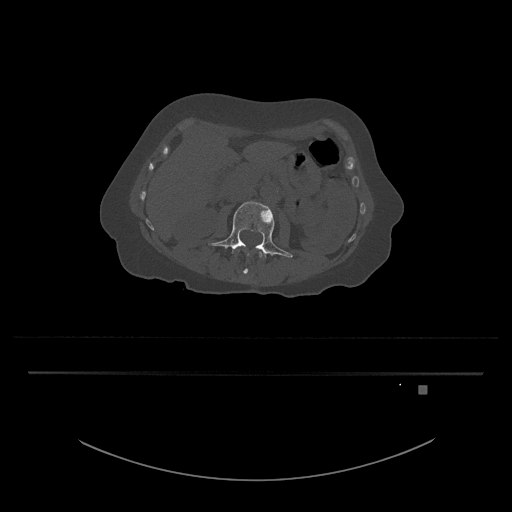
CT including the spine, one axial slice; position 437 of 797 along the scan axis; reconstruction kernel Br40s/3; bone window (W 1800 / L 400 HU); 0.5 mm slice thickness; 512 × 512 image matrix, field of view 500 × 500 mm. Patient: female, 57 years. Case-level facts recorded for this patient, not image findings: primary cancer: cervical.
Structures marked on this image (semi-automatically segmented with operator editing):
- L3 vertebra: bounding box <208,201,293,258> (left, top, right, bottom; pixels)